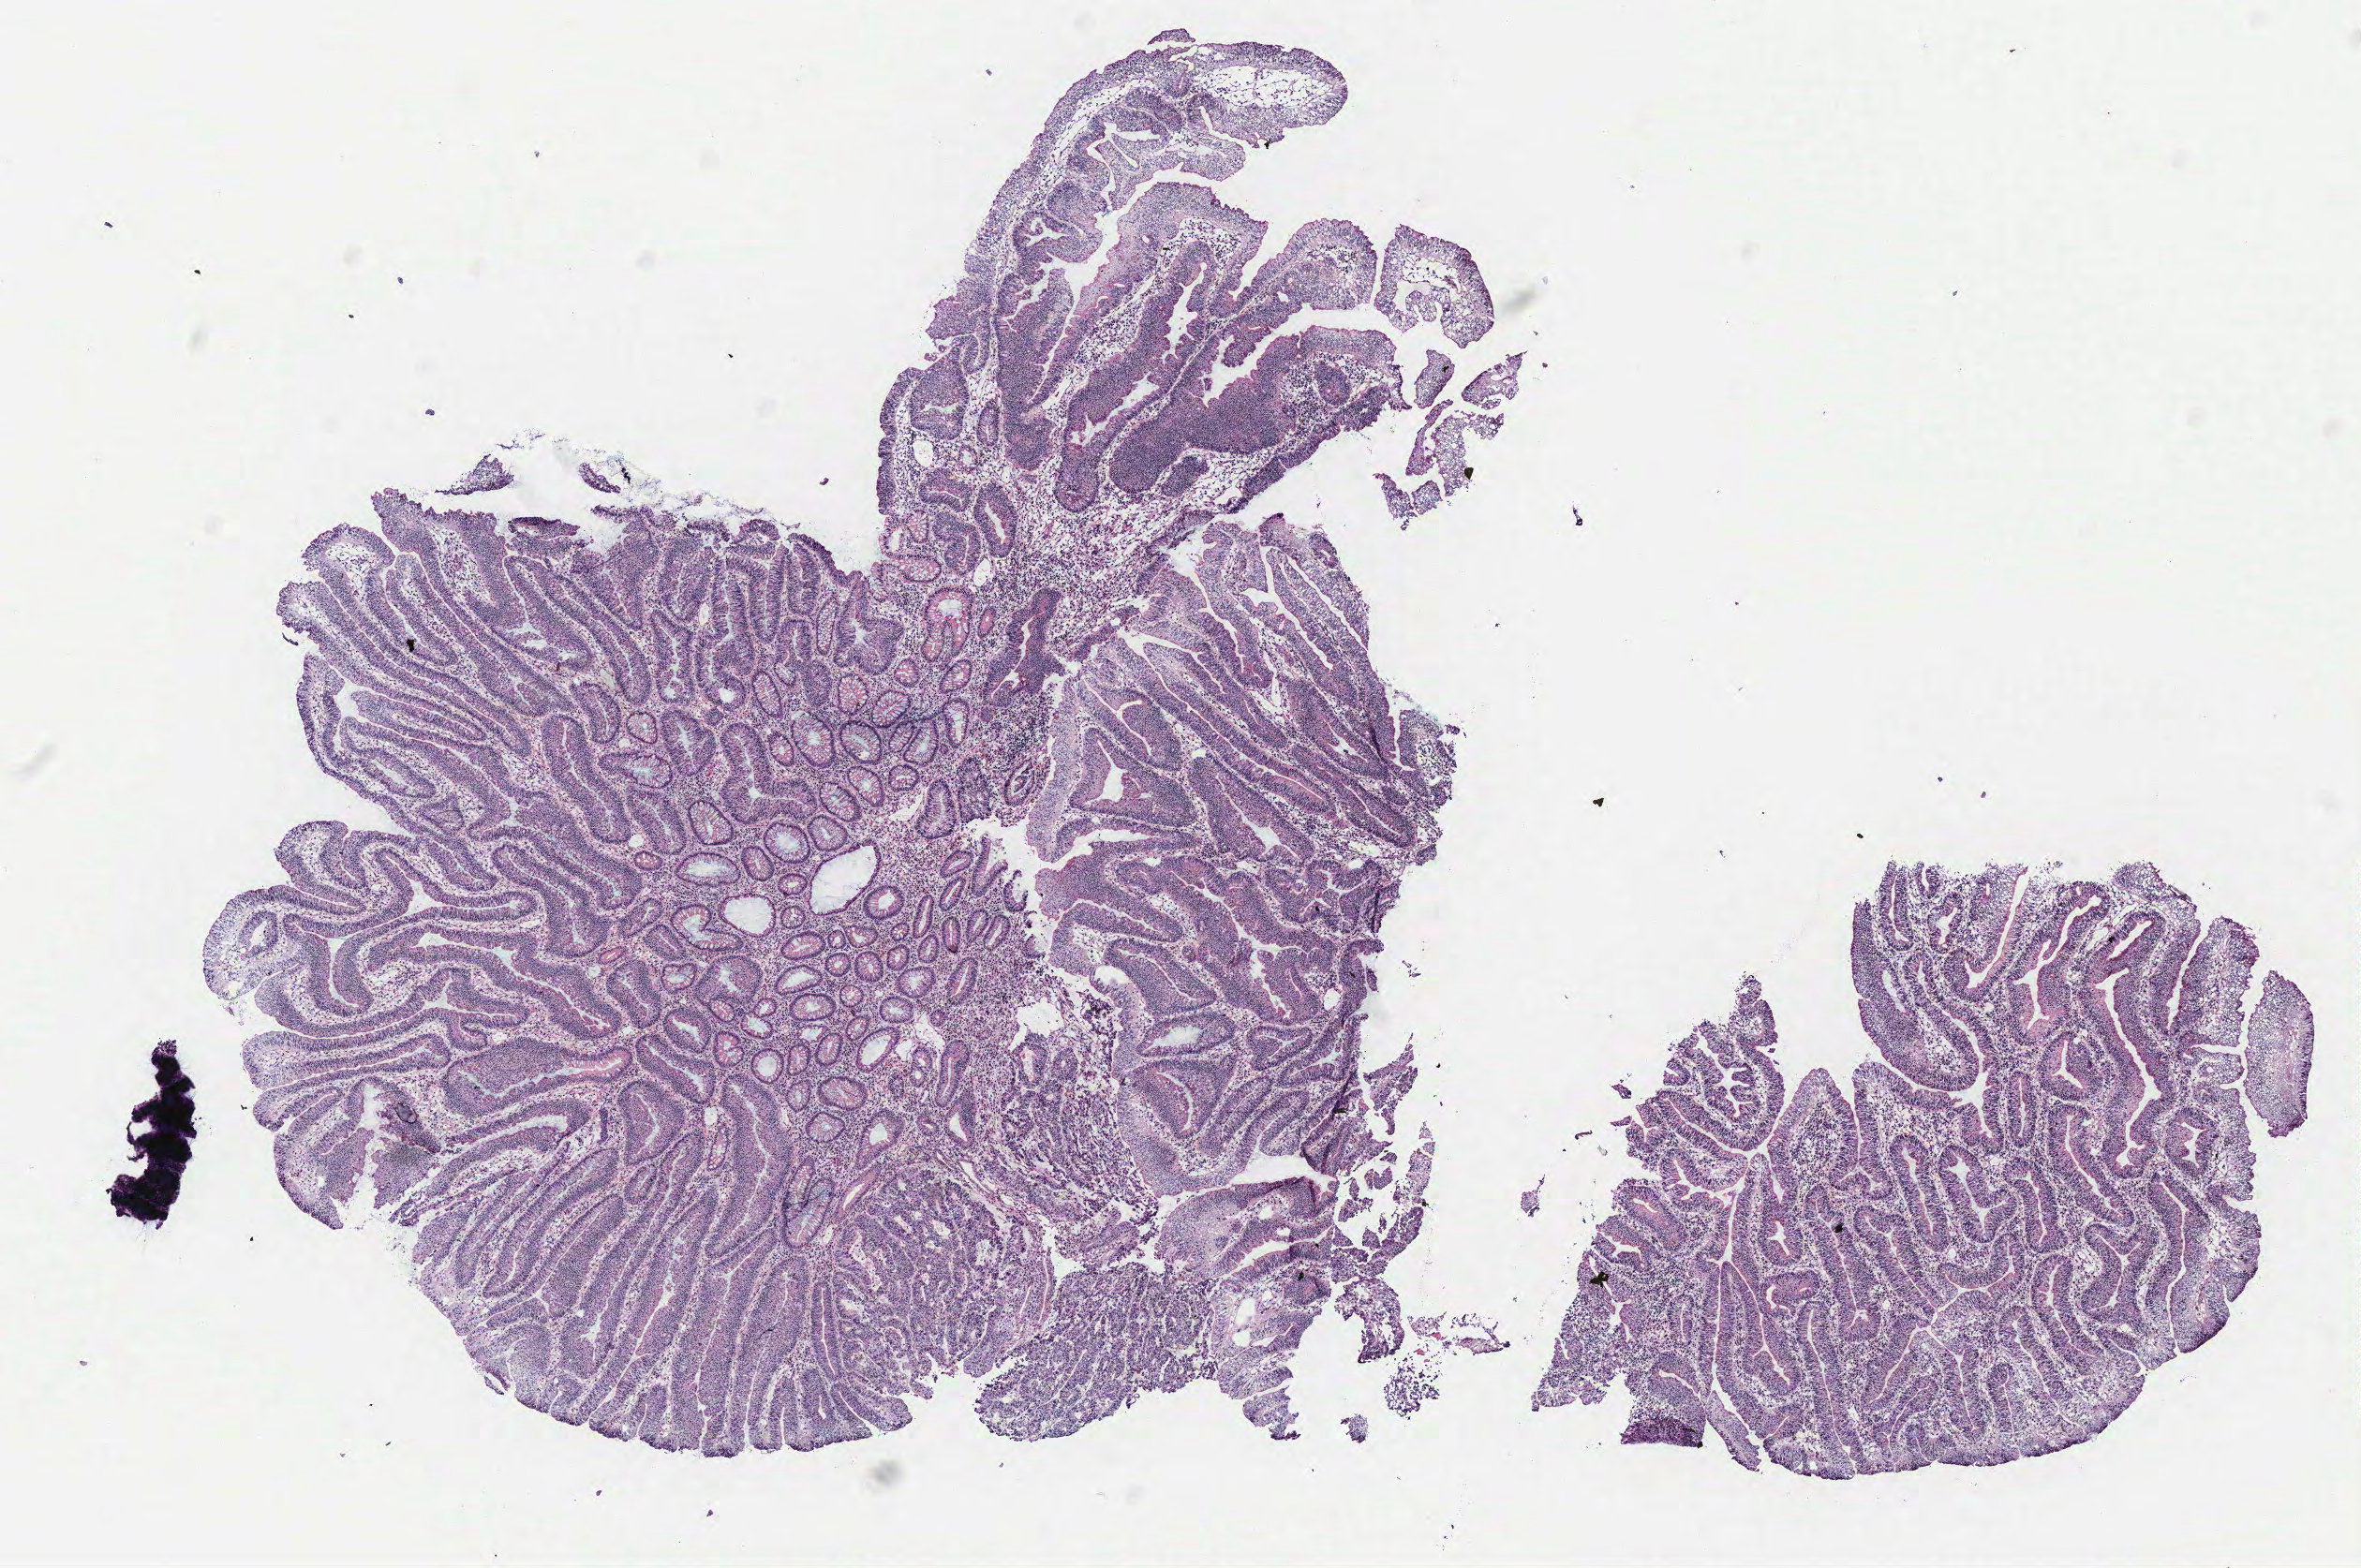
Whole-slide histology image, H&E, a low-resolution overview of the entire scanned area, about 10.1 x 6.7 mm; colon, normal (non-tumour) tissue. Female, 61 y/o.
* this section: normal (non-tumour) tissue from the same patient
* patient diagnosis: Adenocarcinoma, NOS